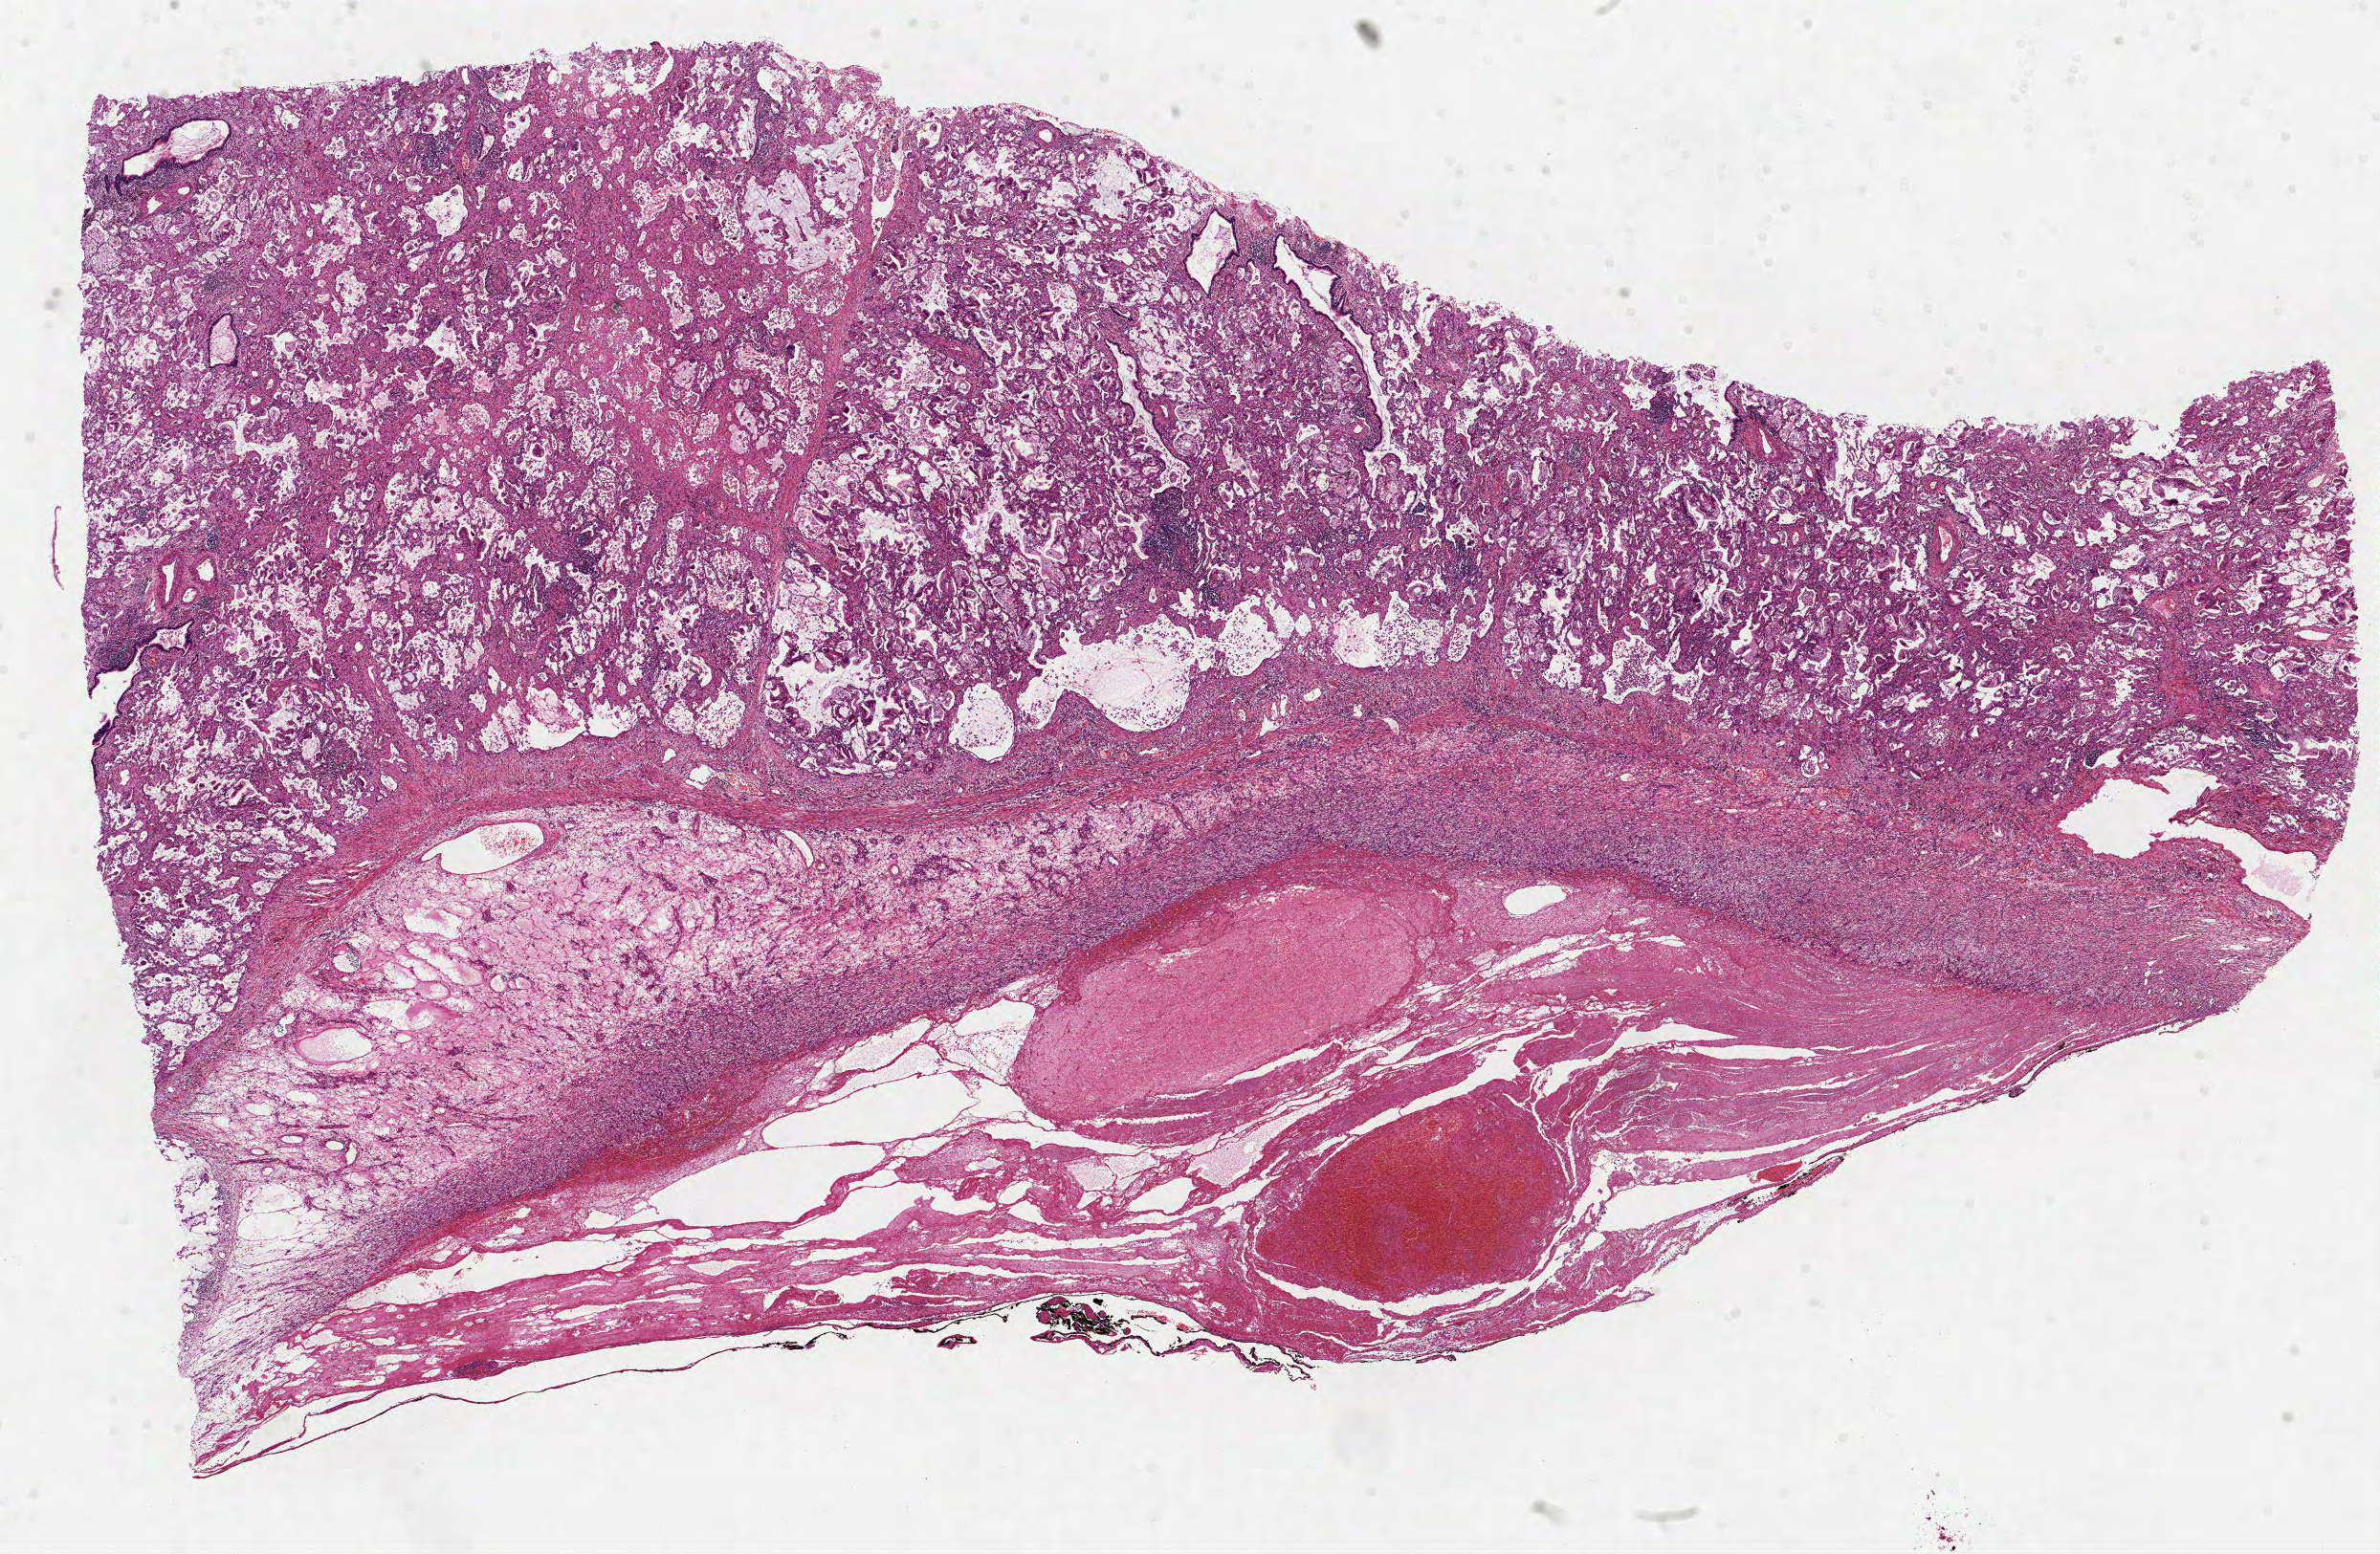
Digitized H&E tissue section (whole slide), low-resolution overview of the scanned area, about 20.1 x 13.1 mm (from a 40x scan); formalin-fixed paraffin-embedded (FFPE) diagnostic section; lung, primary tumour sample. Female, age 66 years at initial diagnosis.
Diagnosis: Bronchio-alveolar carcinoma, mucinous. AJCC pathologic stage: IB (6th edition). Laterality: left.